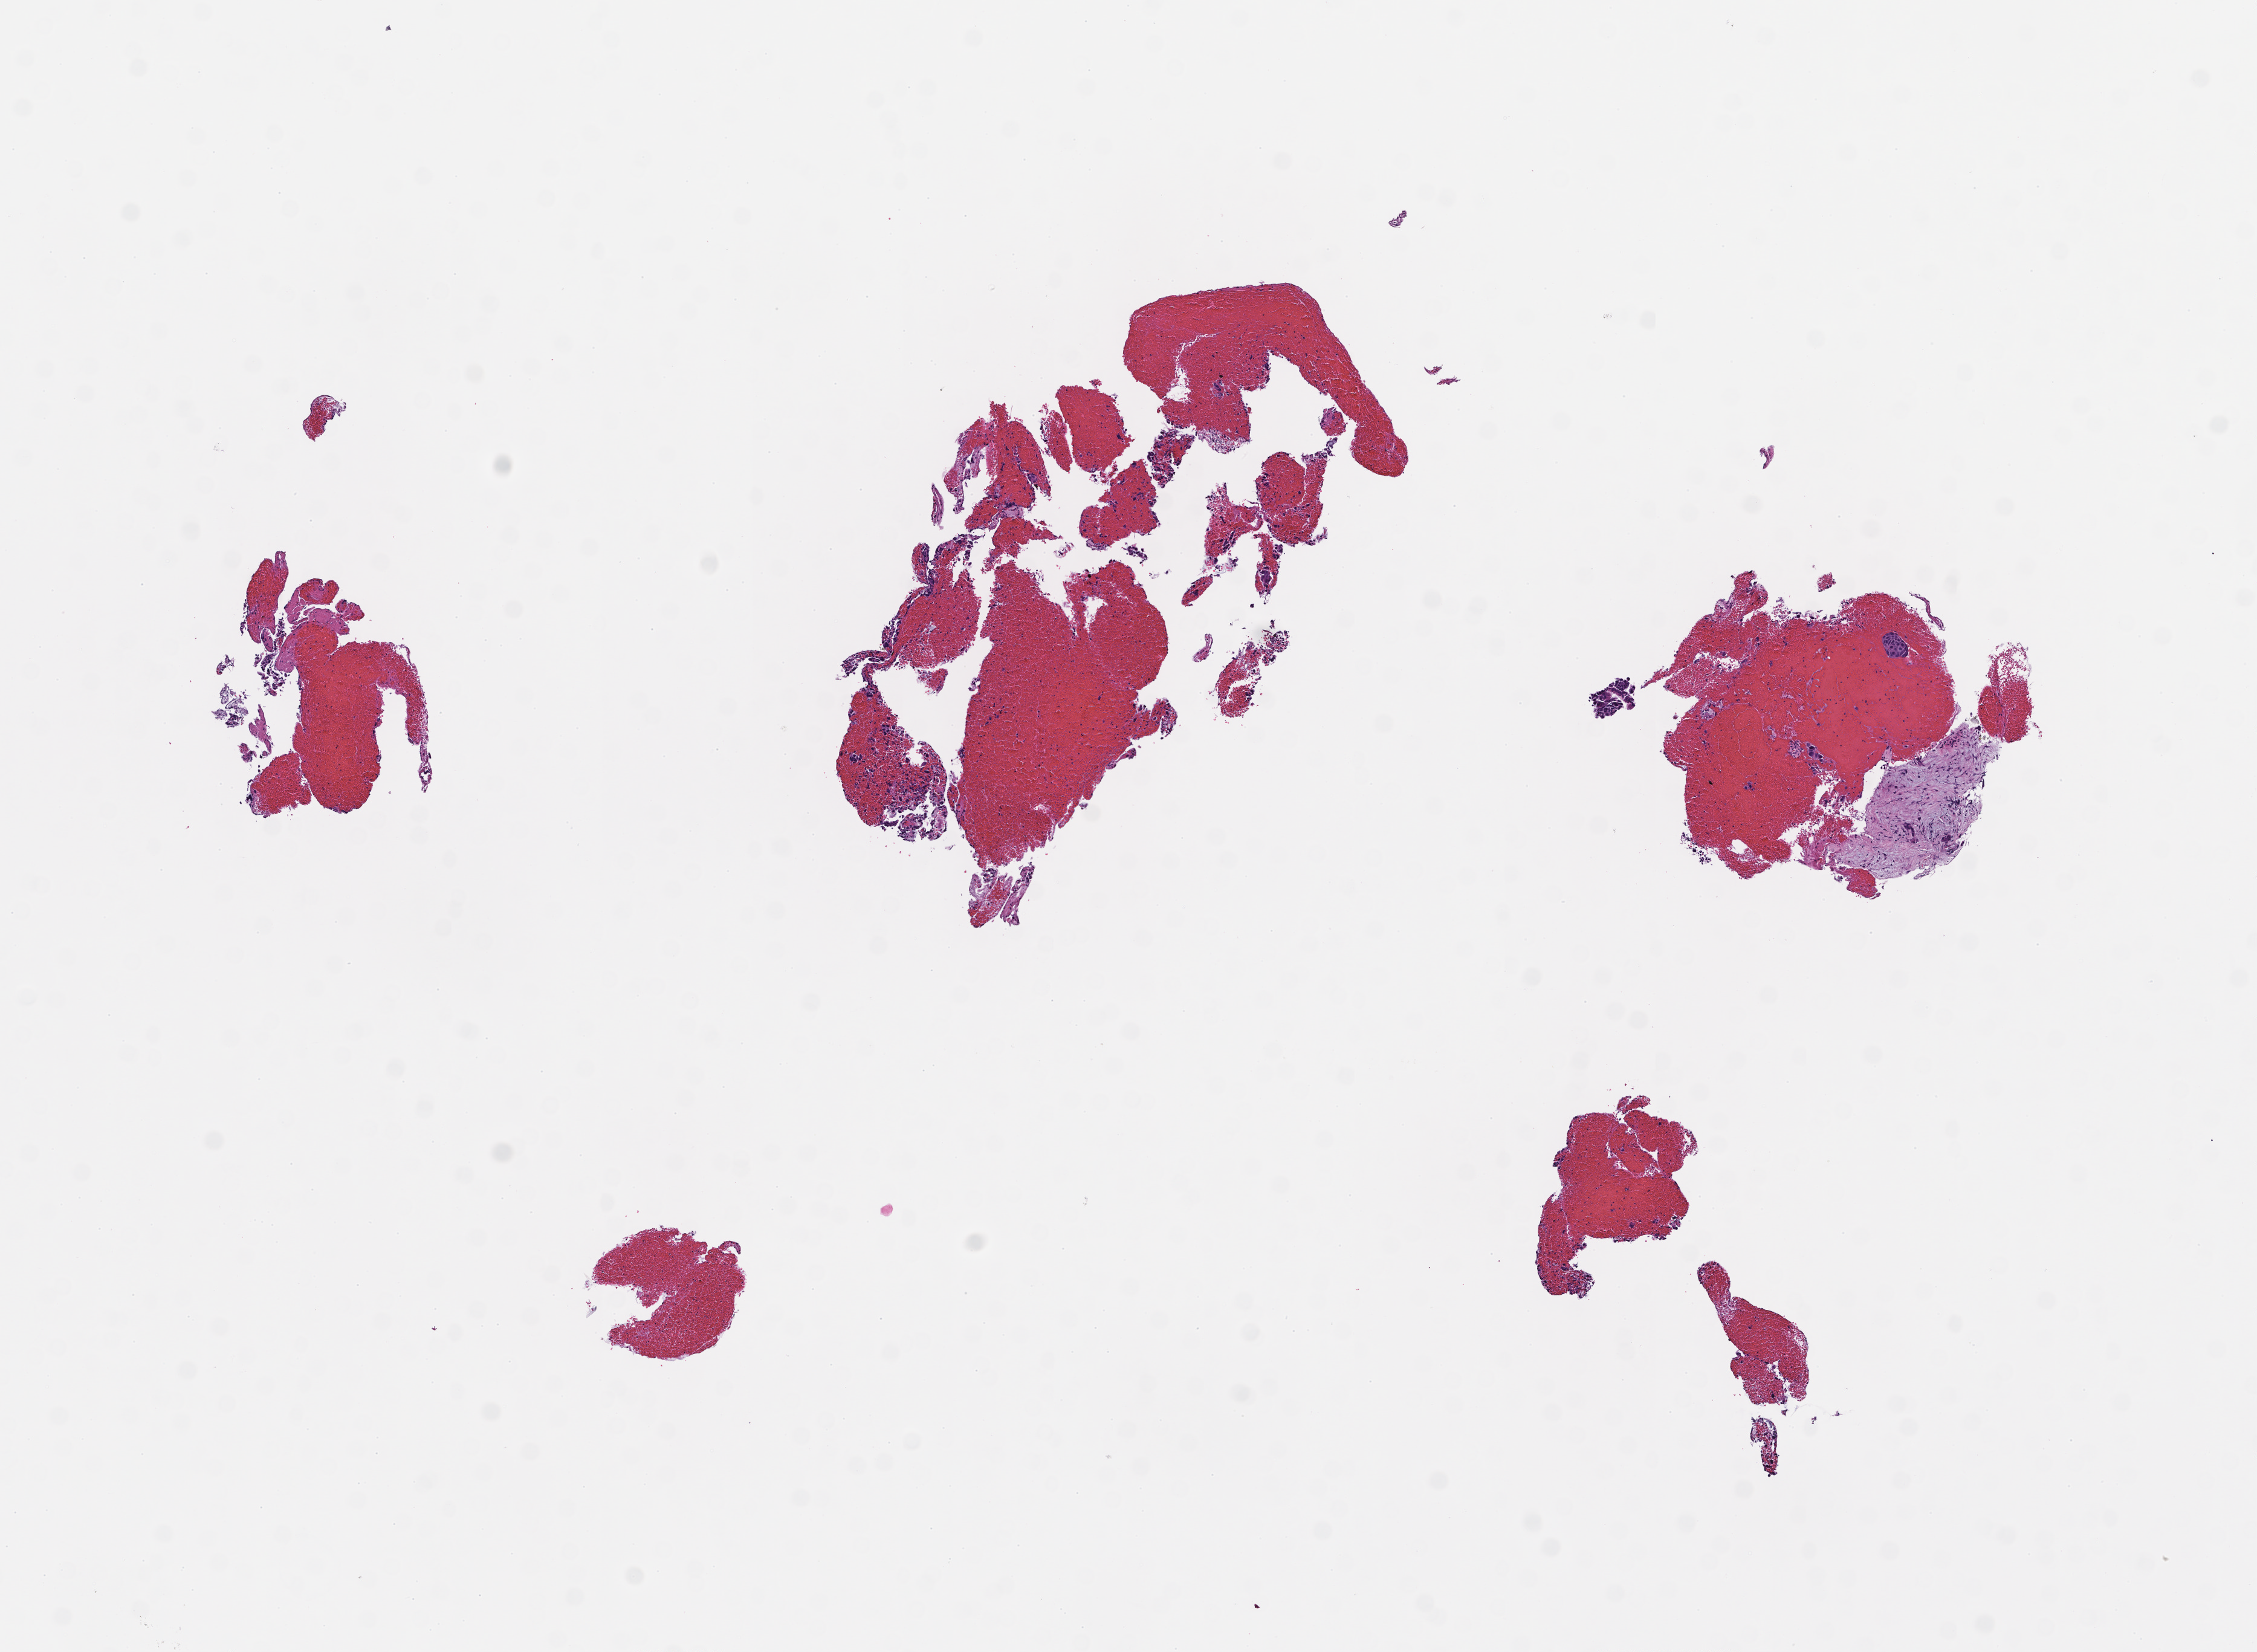
Whole-slide image, H&E stain, low-resolution overview of the scanned area, about 7.5 x 5.5 mm. Formalin-fixed, paraffin-embedded (FFPE) tissue. Tissue site: lung. Specimen time point: collected at baseline (before treatment). Male patient.
This section: primary tumor. Diagnosis: Non-Small Cell Lung Carcinoma.